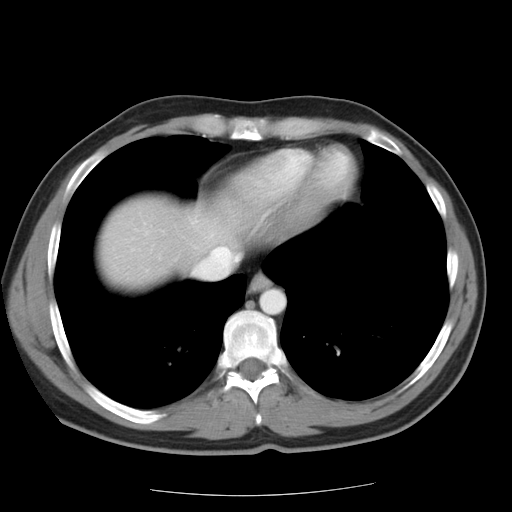
Contrast-enhanced abdominal CT, one axial slice; 120 kVp; soft-tissue window (W 400 / L 40 HU); 7.5 mm slice thickness; 512 × 512 image matrix, field of view 359 × 359 mm. Male patient, age 41 years. From the clinical record (not read from this slice): diagnosis: colorectal cancer liver metastases, imaged before liver resection; multiple liver metastases: no; largest metastasis: 2.7 cm.
Outlined on this slice (manually delineated by an expert):
- liver: bounding box (x1, y1, x2, y2) in pixels: (102, 199, 230, 284)
- planned liver remnant (the part of the liver to remain after resection): (102, 200, 230, 283)